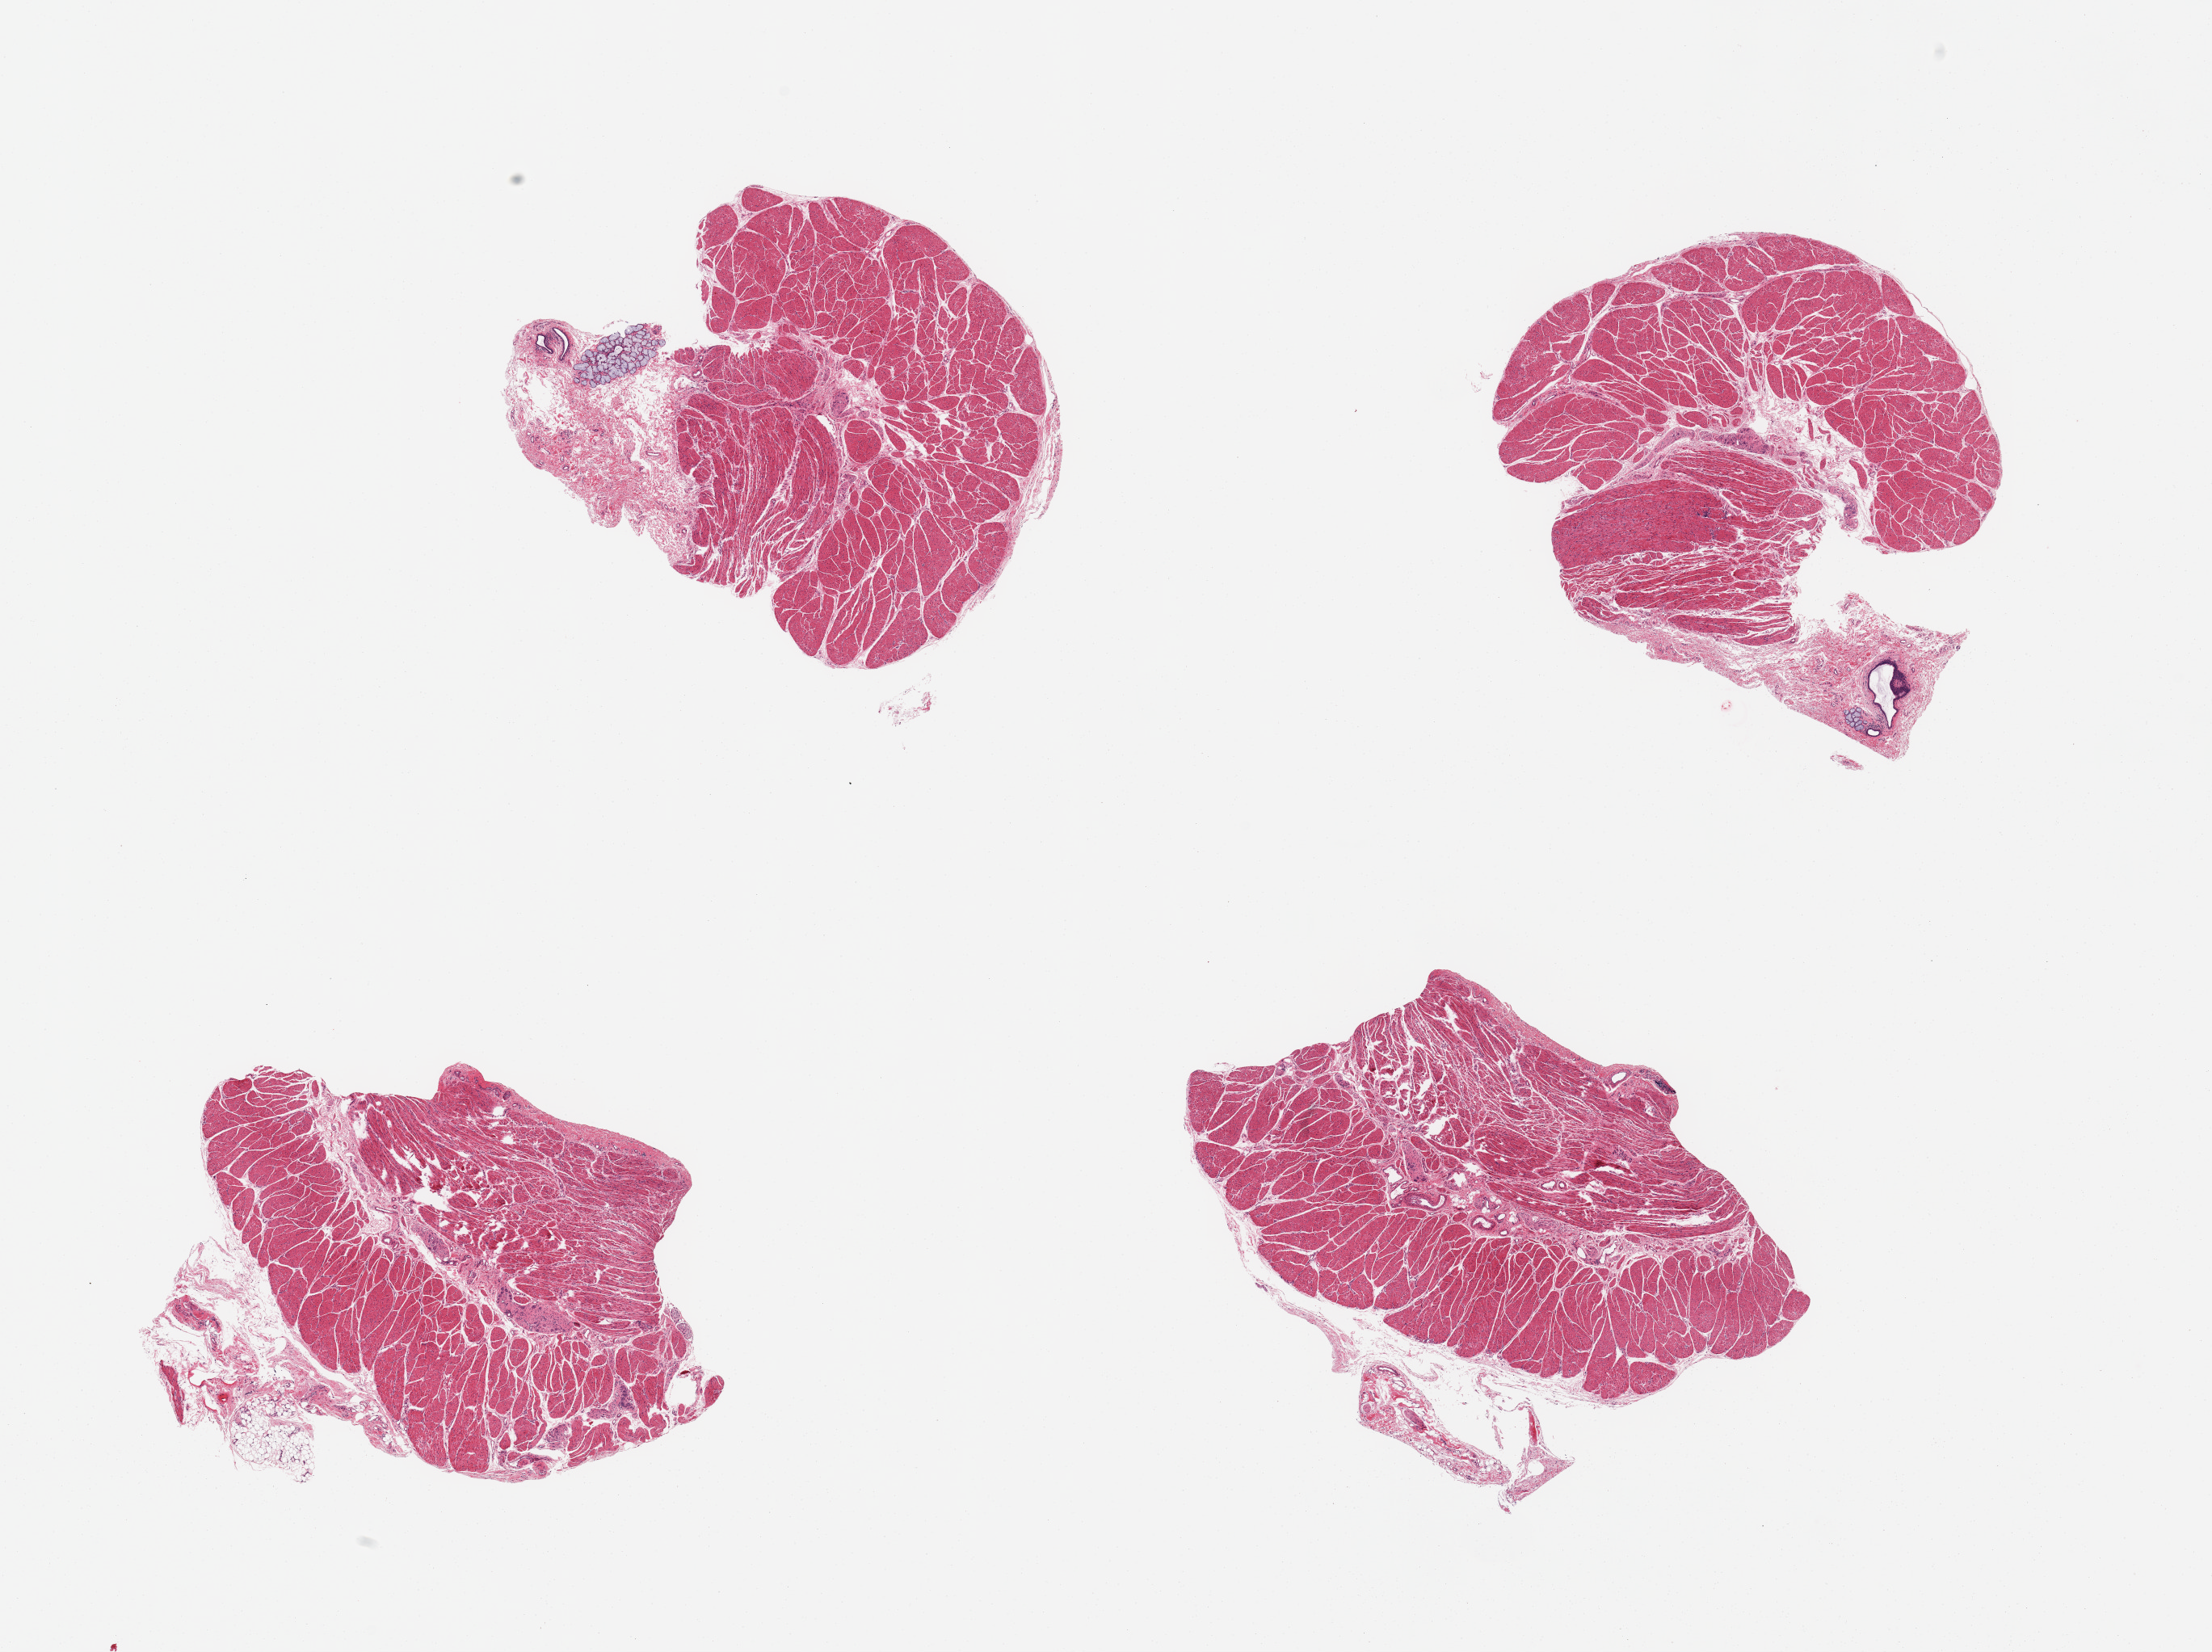
H&E whole-slide image, brightfield, whole scanned area (about 21.7 x 16.2 mm) shown as a low-resolution overview. PAXgene-fixed, paraffin-embedded tissue. Target tissue: esophageal muscle. Tissue donor sample. Male donor.
Pathologist's review note for this sample: 4 pieces; submucosal gland in 2 pieces.